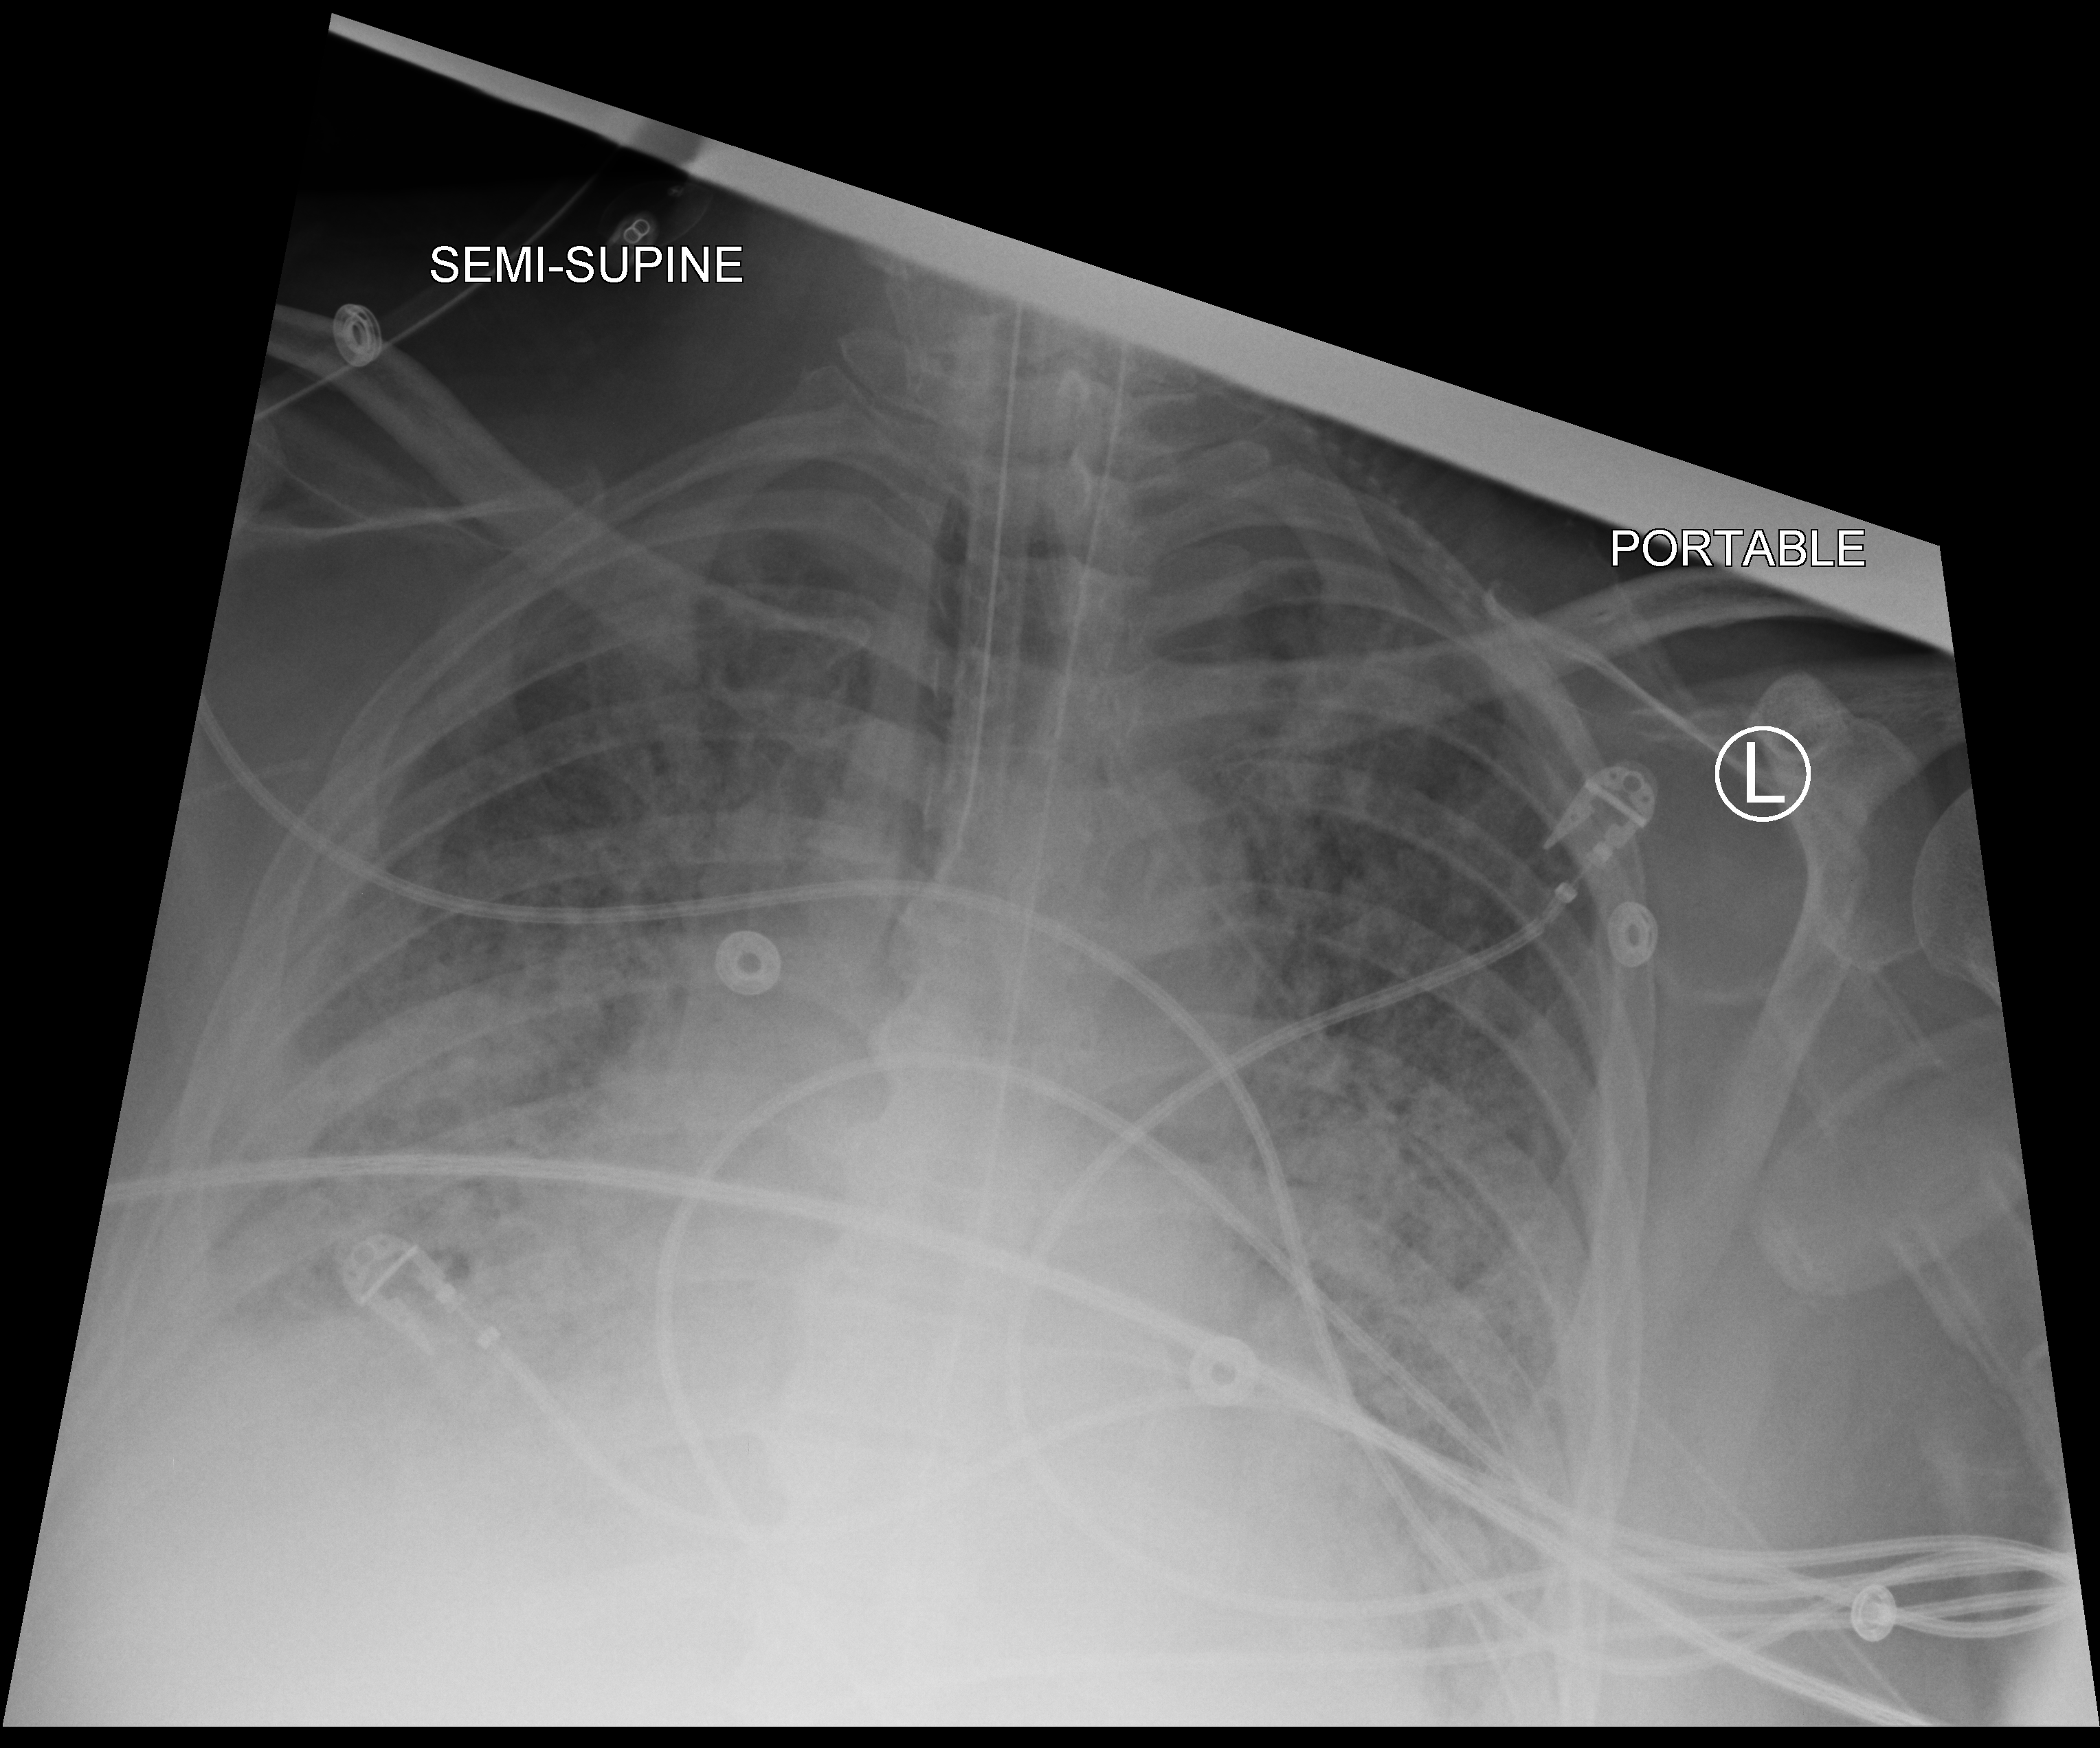
Chest X-ray (portable); anteroposterior (AP) projection. Patient hospitalised with COVID-19; male, aged 60–74 years.
From the hospital-stay record, not from the radiograph (when in the stay this image was taken is not recorded):
- length of hospital stay: 40 days
- hypertension (admission record): yes
- admitted to intensive care during this hospital stay: yes